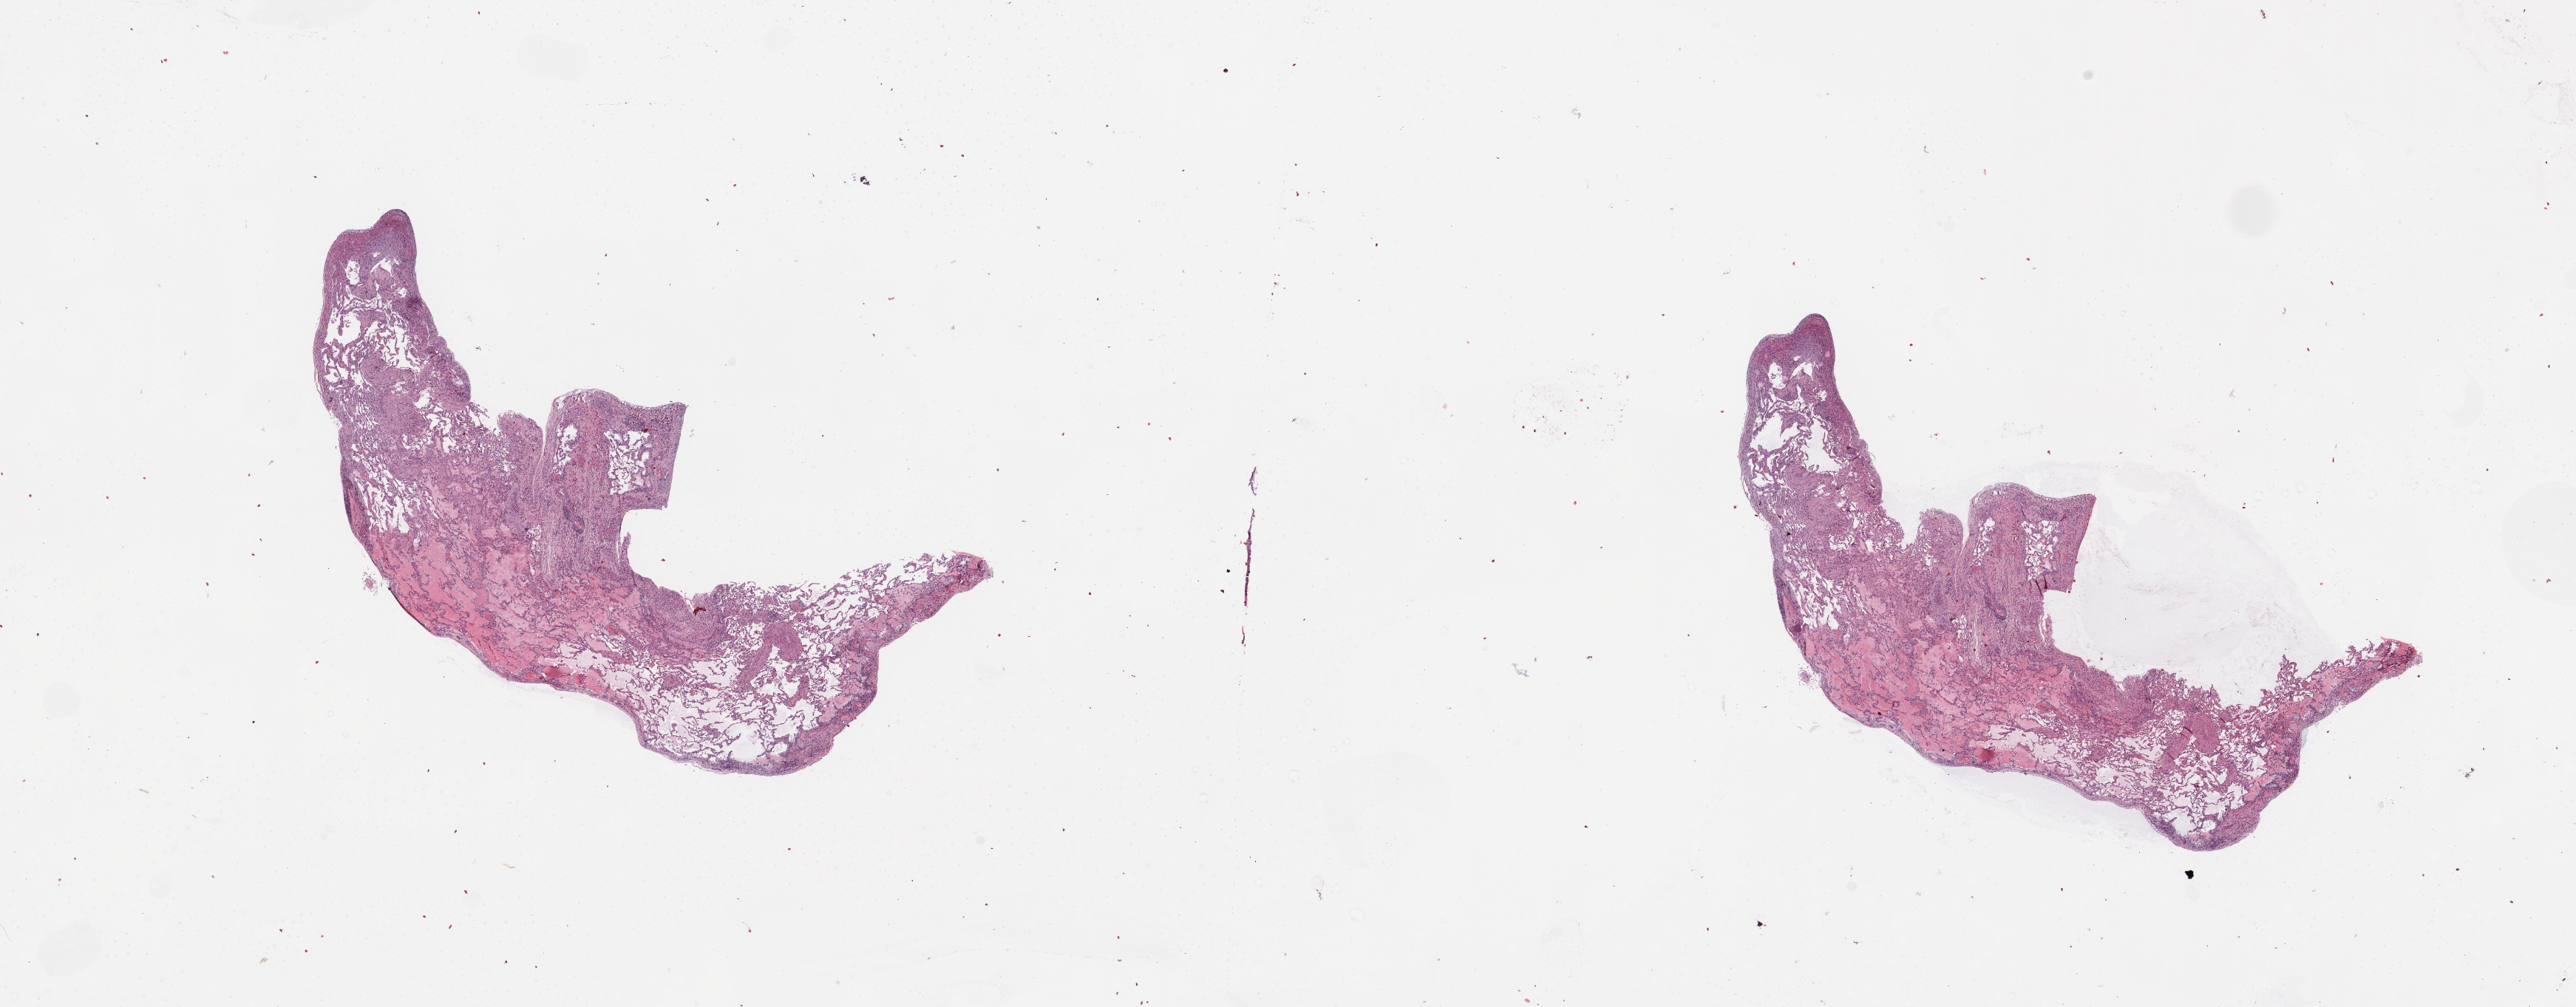
Whole-slide histology image, Hematoxylin and eosin (H&E) stained — a low-resolution overview of the entire scanned area, about 27.6 x 10.8 mm; normal (non-tumour) tissue sample, lung. Male, 70 y/o.
This section: normal (non-tumour) tissue from the same patient. Patient diagnosis: Squamous cell carcinoma, NOS.